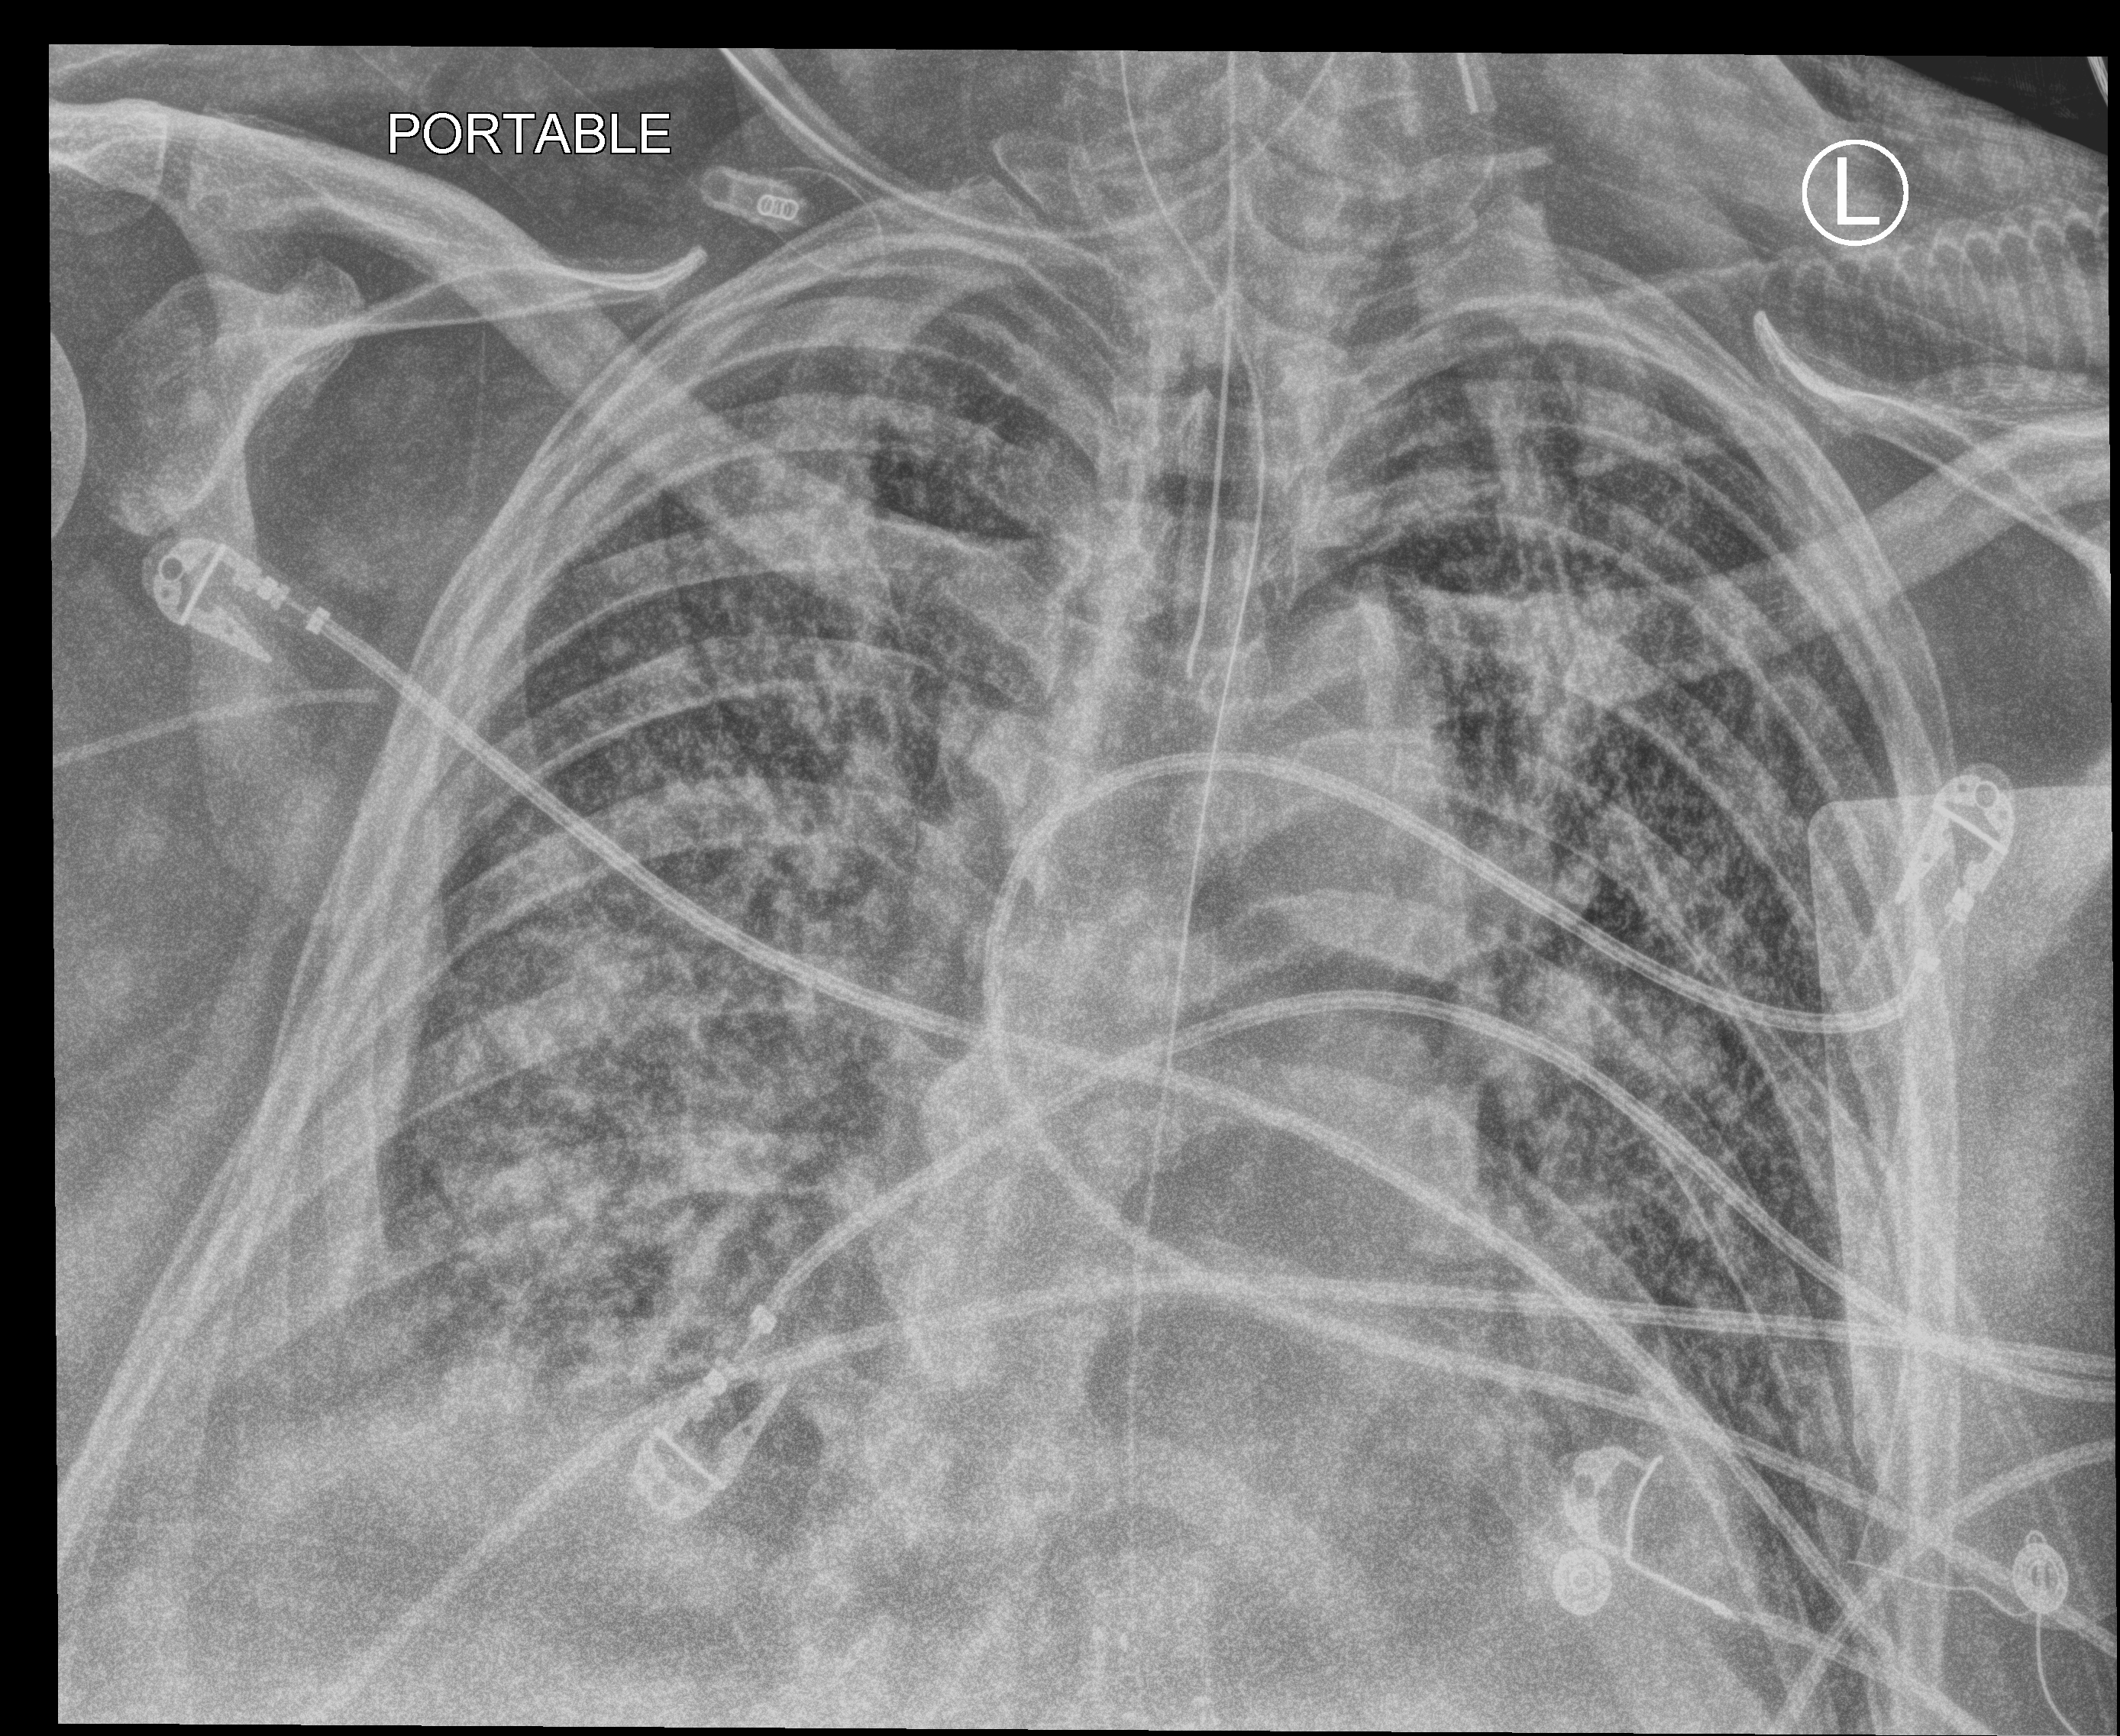
Portable chest radiograph. Patient hospitalised with COVID-19; male, aged 60–74 years.
Admission-level facts for this patient (not findings on this image; timing relative to this image not recorded):
- admitted to intensive care during this hospital stay: yes